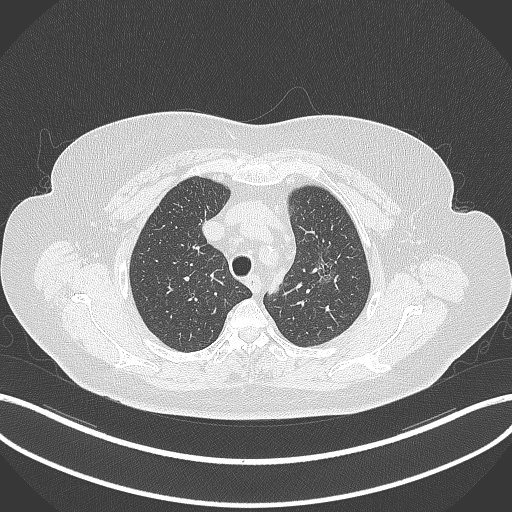
Chest CT, one axial slice; reconstruction kernel B70f; 120 kVp; lung window (W 1500 / L -600 HU); 1 mm slice thickness; 512 × 512 image matrix, field of view 400 × 400 mm. Female patient, age 70 years. Case-level facts recorded for this patient, not image findings: clinical TNM (as recorded): T1c N0 M0.
Outlined on this slice (rectangle marked by the reading radiologist):
- lung tumour (recorded histology: adenocarcinoma): bounding box <312,254,339,286> (left, top, right, bottom; pixels)